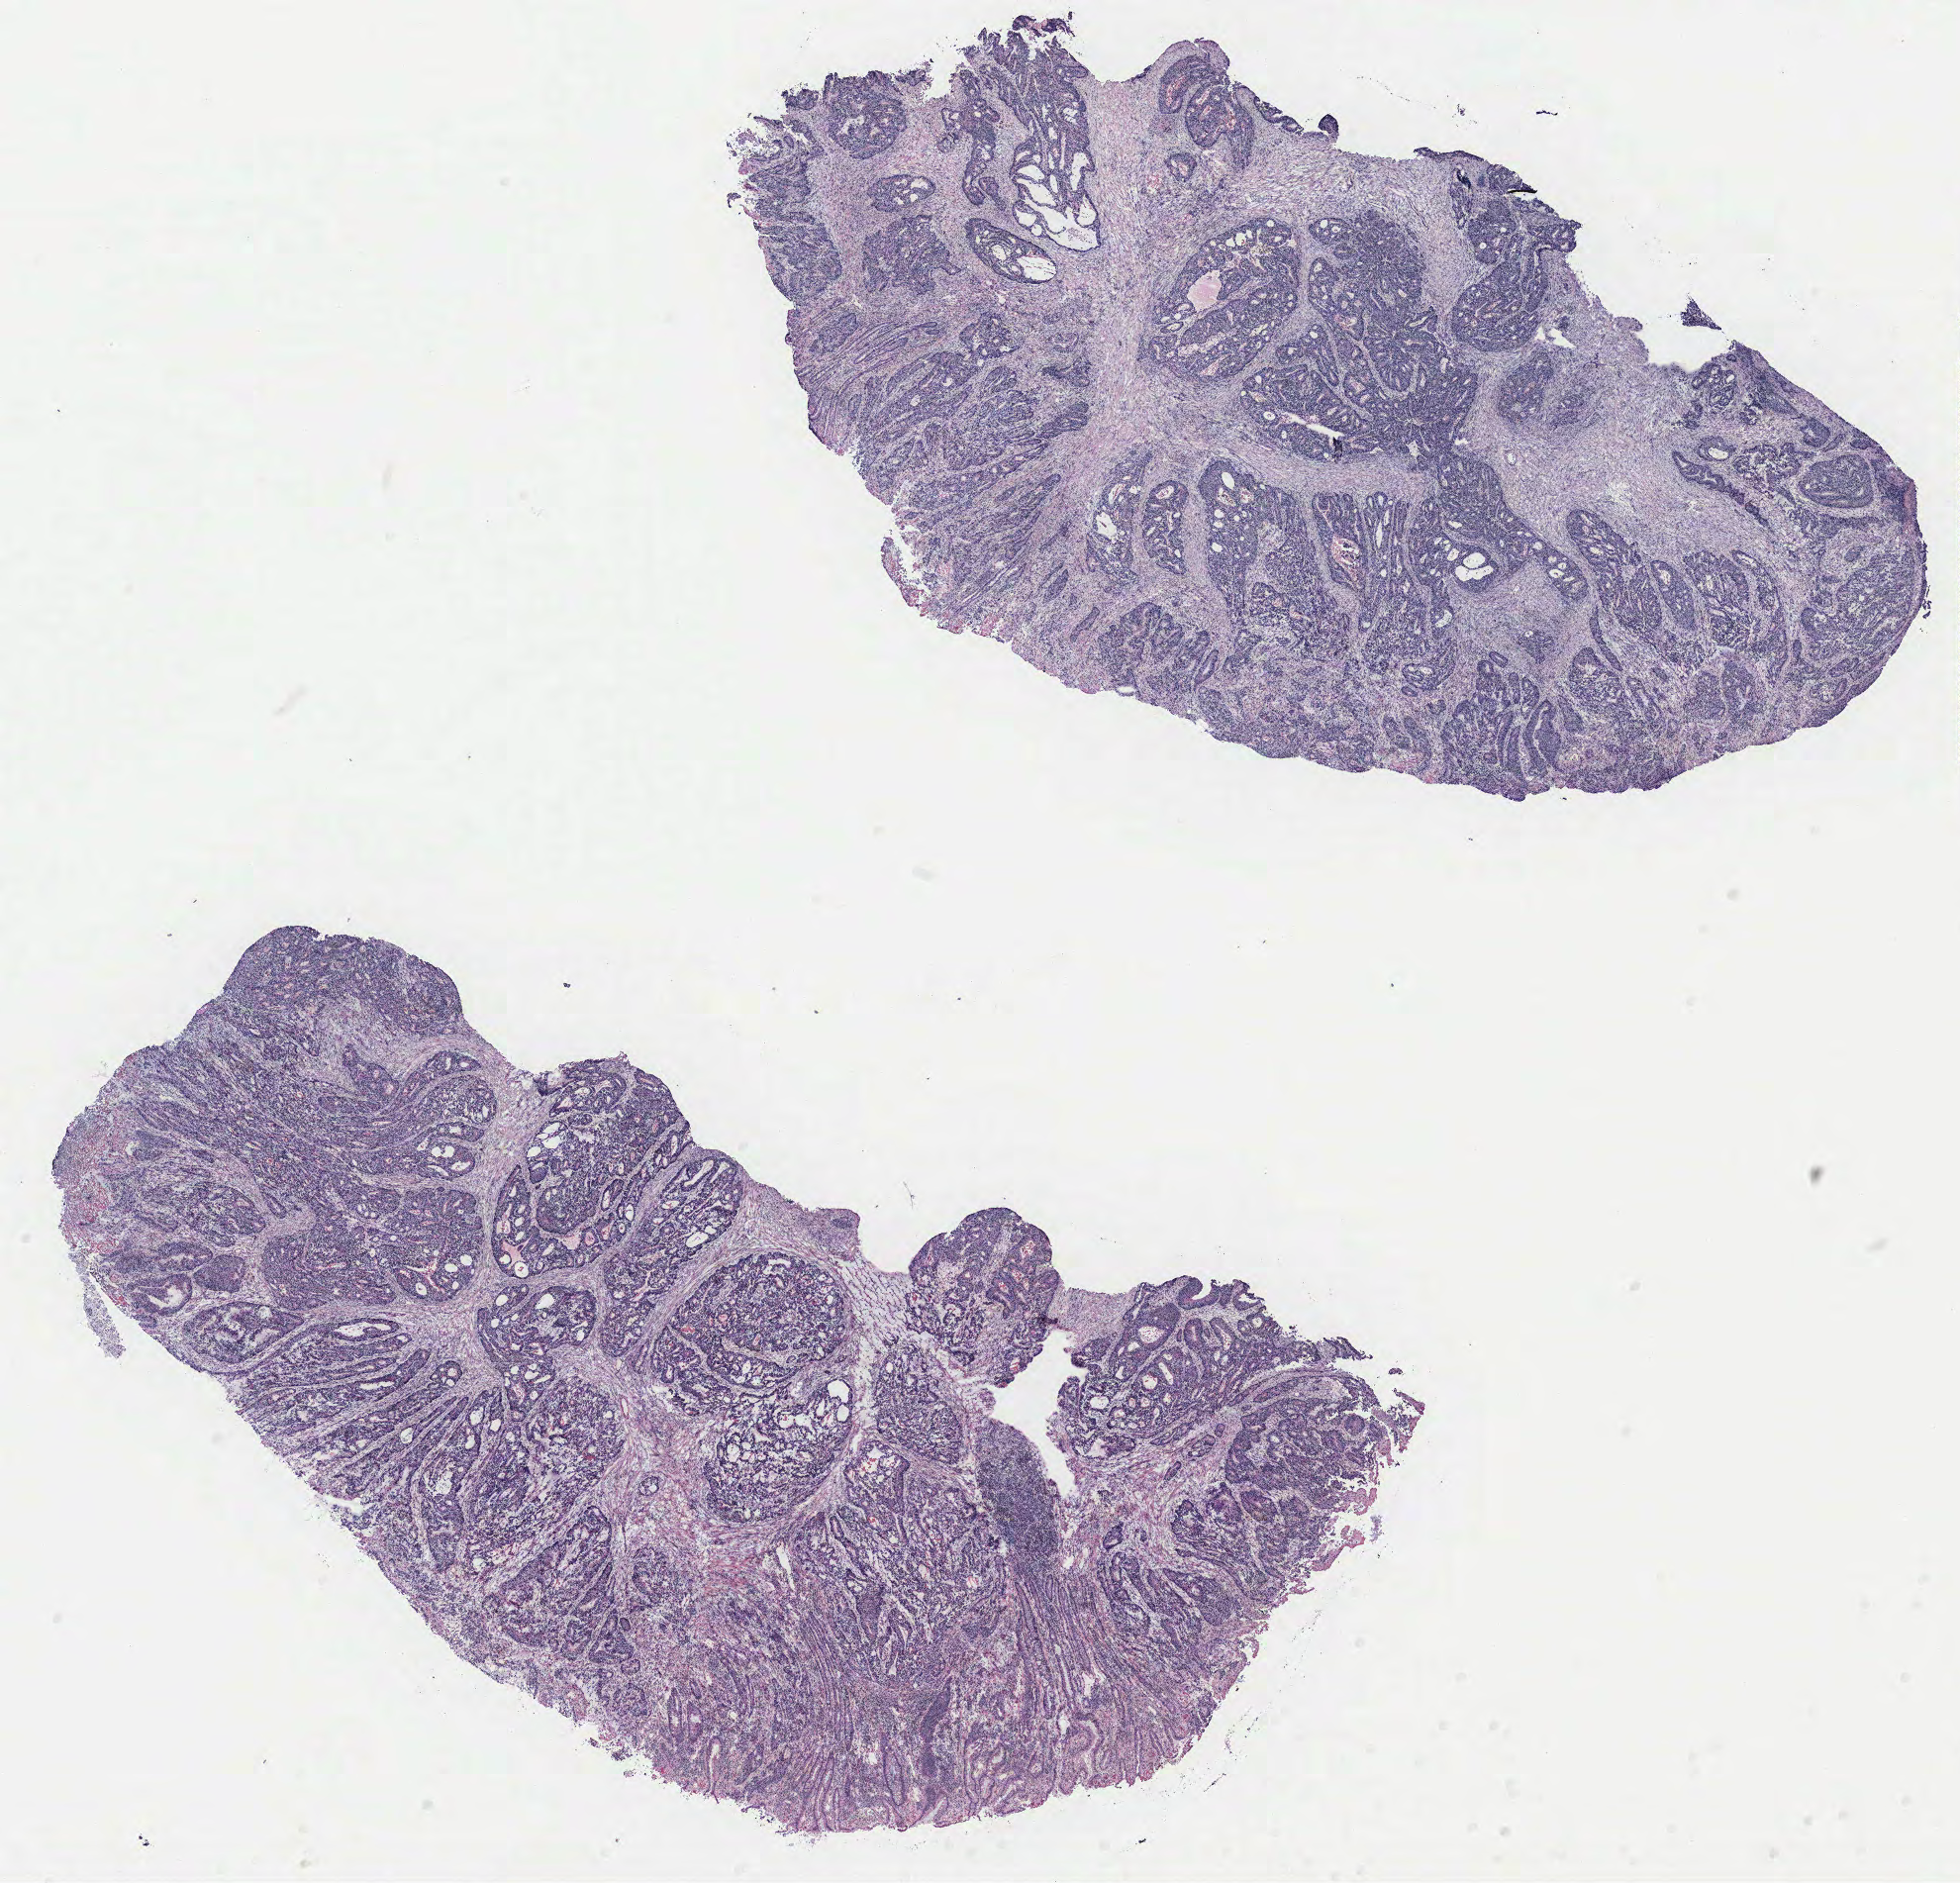
Whole-slide histology image, H&E — whole scanned area (about 15.8 x 15.2 mm, acquisition: 40x scan) shown as a low-resolution overview. Tumour tissue sample, colon. 40-year-old female patient.
Primary tumour site (as recorded): colon. Patient diagnosis (cohort enrolment): colon cancer (colon).